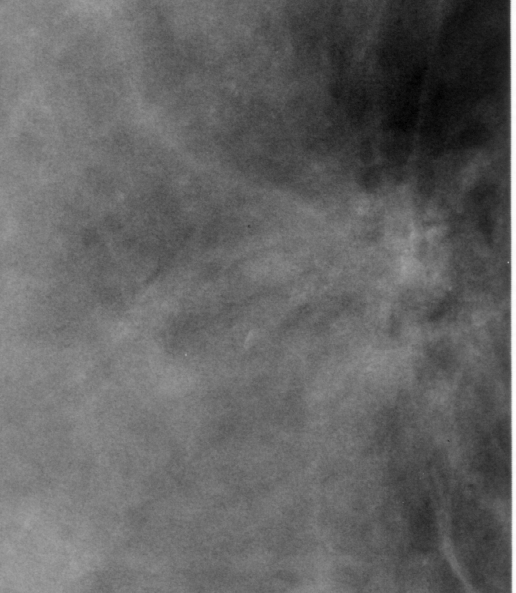
Region of interest cut from a scanned film mammogram (one marked finding), right breast, CC view.
Calcifications, morphology punctate / pleomorphic, distribution clustered; BI-RADS assessment category 4; pathology result (as recorded, not read from the image): malignant.